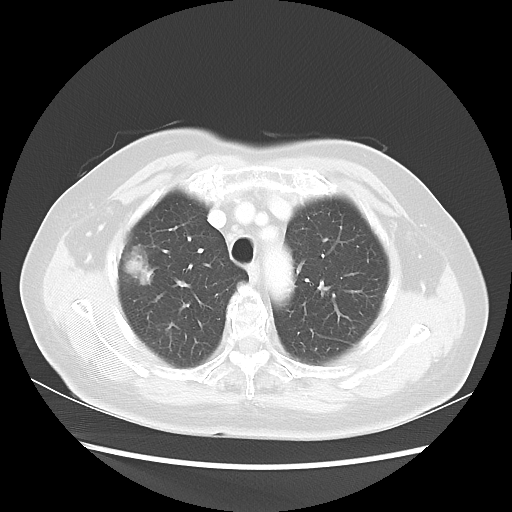
Chest CT, one axial slice. Slice 37 of 48 in the series (ordered by position). Reconstruction kernel LUNG. 100 kVp. Lung window (W 1500 / L -600 HU). 5 mm slice thickness. 512 × 512 image matrix. Female patient, age 75 years. From the clinical record (not read from this slice): clinical TNM (as recorded): T1c N0 M0.
Outlined on this slice (bounding box drawn by a radiologist):
- lung tumour (recorded histology: adenocarcinoma): box from (x=125, y=244) to (x=163, y=292) px